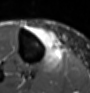
MRI of an extremity soft-tissue mass, one axial slice. Slice 27 of 60 in the series (ordered by position). STIR. MR volume resampled by the dataset authors to the PET/CT grid (not the native acquisition matrix). 3.27 mm slice thickness. 90 × 93 image matrix. Female patient. Case-level facts recorded for this patient, not image findings: histological type: undifferentiated – high grade; grade: high; site of the primary tumour: right thigh.
Annotated regions visible in this slice (expert contour drawn on MRI and transferred to this co-registered scan by the dataset authors):
- gross tumour volume (mass): bounding box (x1, y1, x2, y2) in pixels: (31, 26, 63, 72)